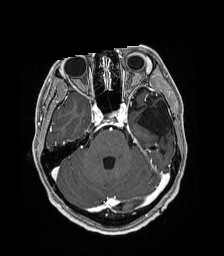
Brain MRI from a brain-tumour surgery series, one axial slice. Slice 125 of 192 in the series (ordered by position). T1-weighted post-contrast. 224 × 256 image matrix, field of view 224 × 256 mm. From the clinical record (not read from this slice): histopathology: Low grade glioma; IDH mutation: no.
Annotated regions visible in this slice (expert manual segmentation):
- previous resection cavity: bounding box [x1, y1, x2, y2] px = [137, 101, 172, 135]